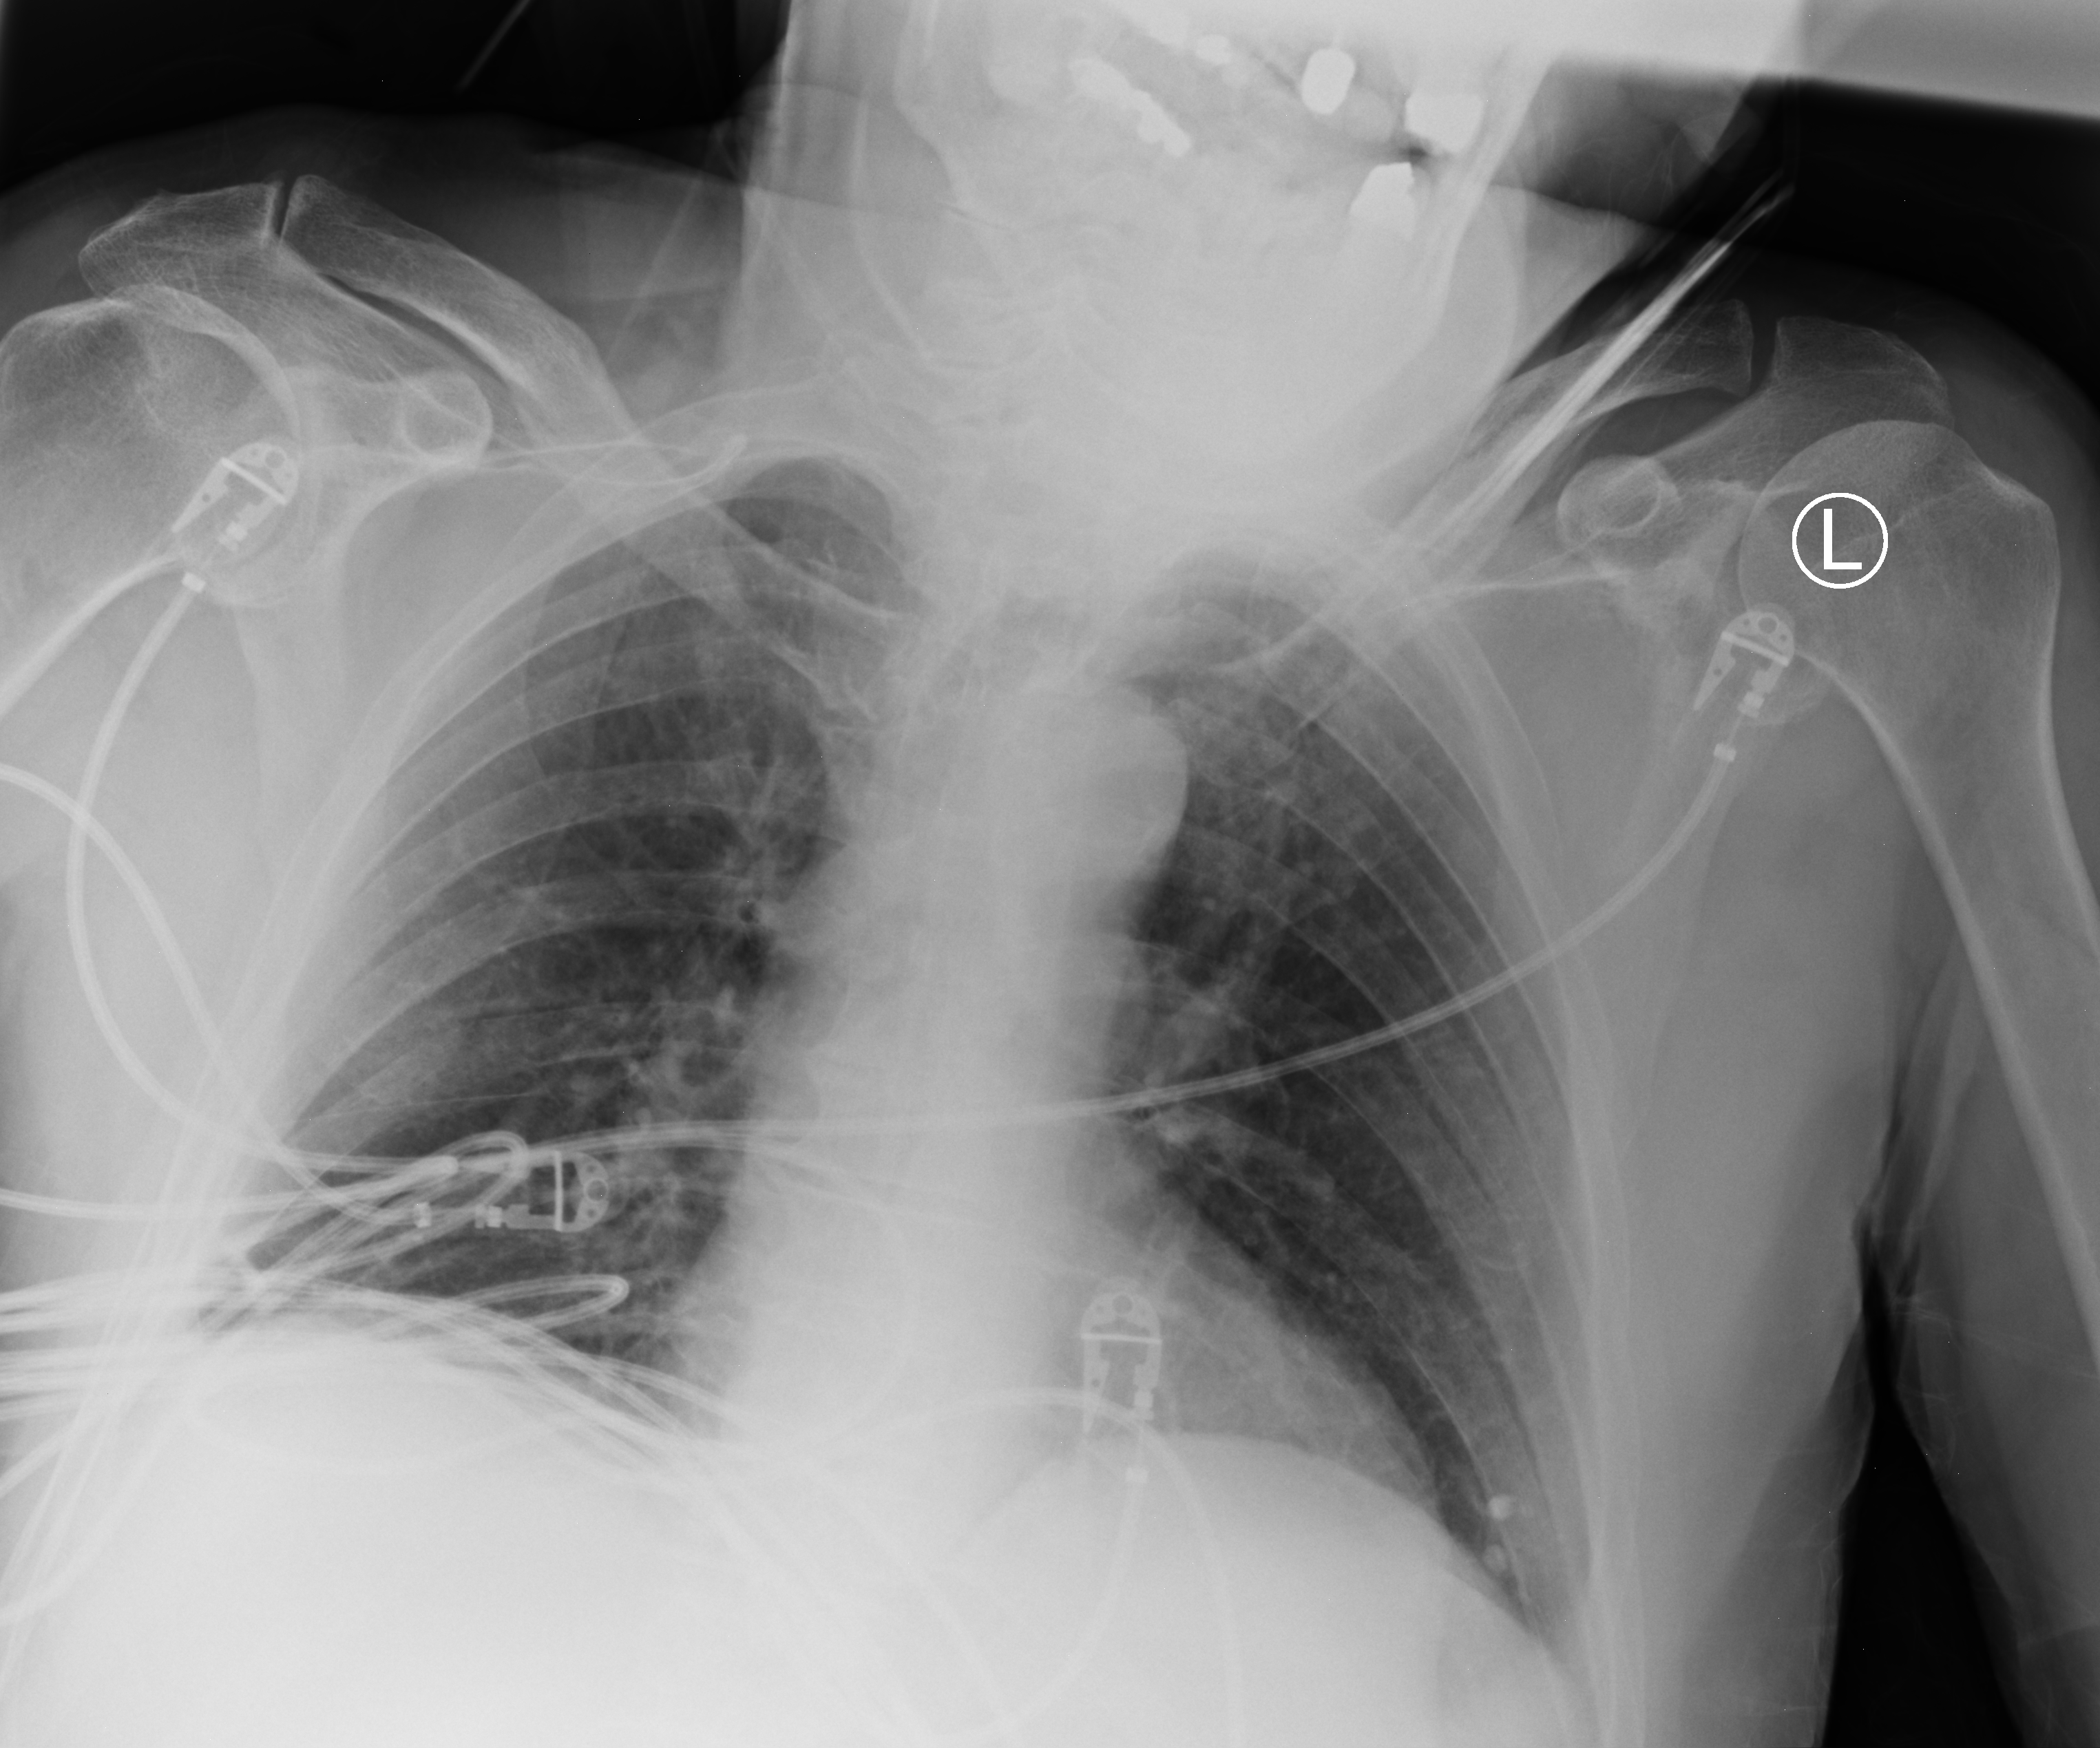
Bedside chest radiograph (computed radiography); anteroposterior (AP) projection. Male patient hospitalised with COVID-19, age 75–90 years.
Hospital-stay facts (about this admission, not read from this image; timing relative to this image not recorded):
- smoking status (admission record): never